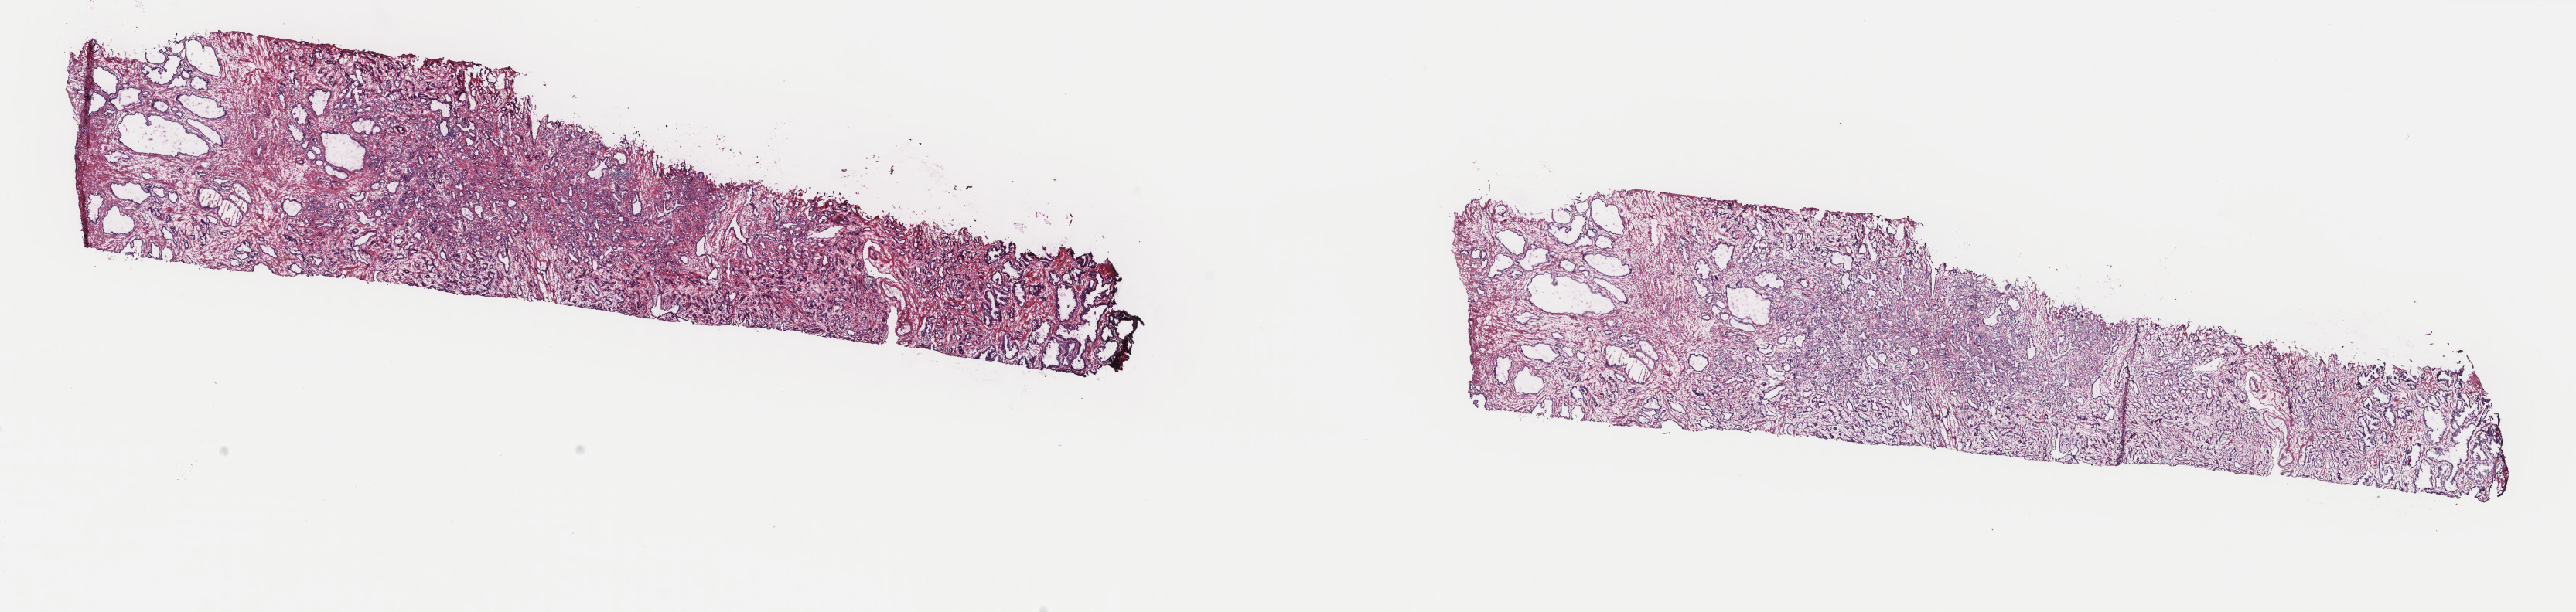
Digitized H&E tissue section (whole slide) — low-resolution overview of the scanned area, about 26.4 x 6.3 mm (acquisition: 40x scan); frozen section from the top of the tissue portion; prostate, primary tumour sample. Patient: male, age at initial diagnosis 53 years. Gleason score: 8 (3+5). Slide review estimates, as recorded: tumour cells 50%, tumour nuclei 70%, normal cells 20%, stromal cells 30%, necrosis 0%. Inflammatory infiltration, as recorded: lymphocyte infiltration 0%, monocyte infiltration 0%, neutrophil infiltration 0%.
Lymph nodes positive (case pathology): 0 of 6 examined. Diagnosis: Adenocarcinoma, NOS (prostate gland).